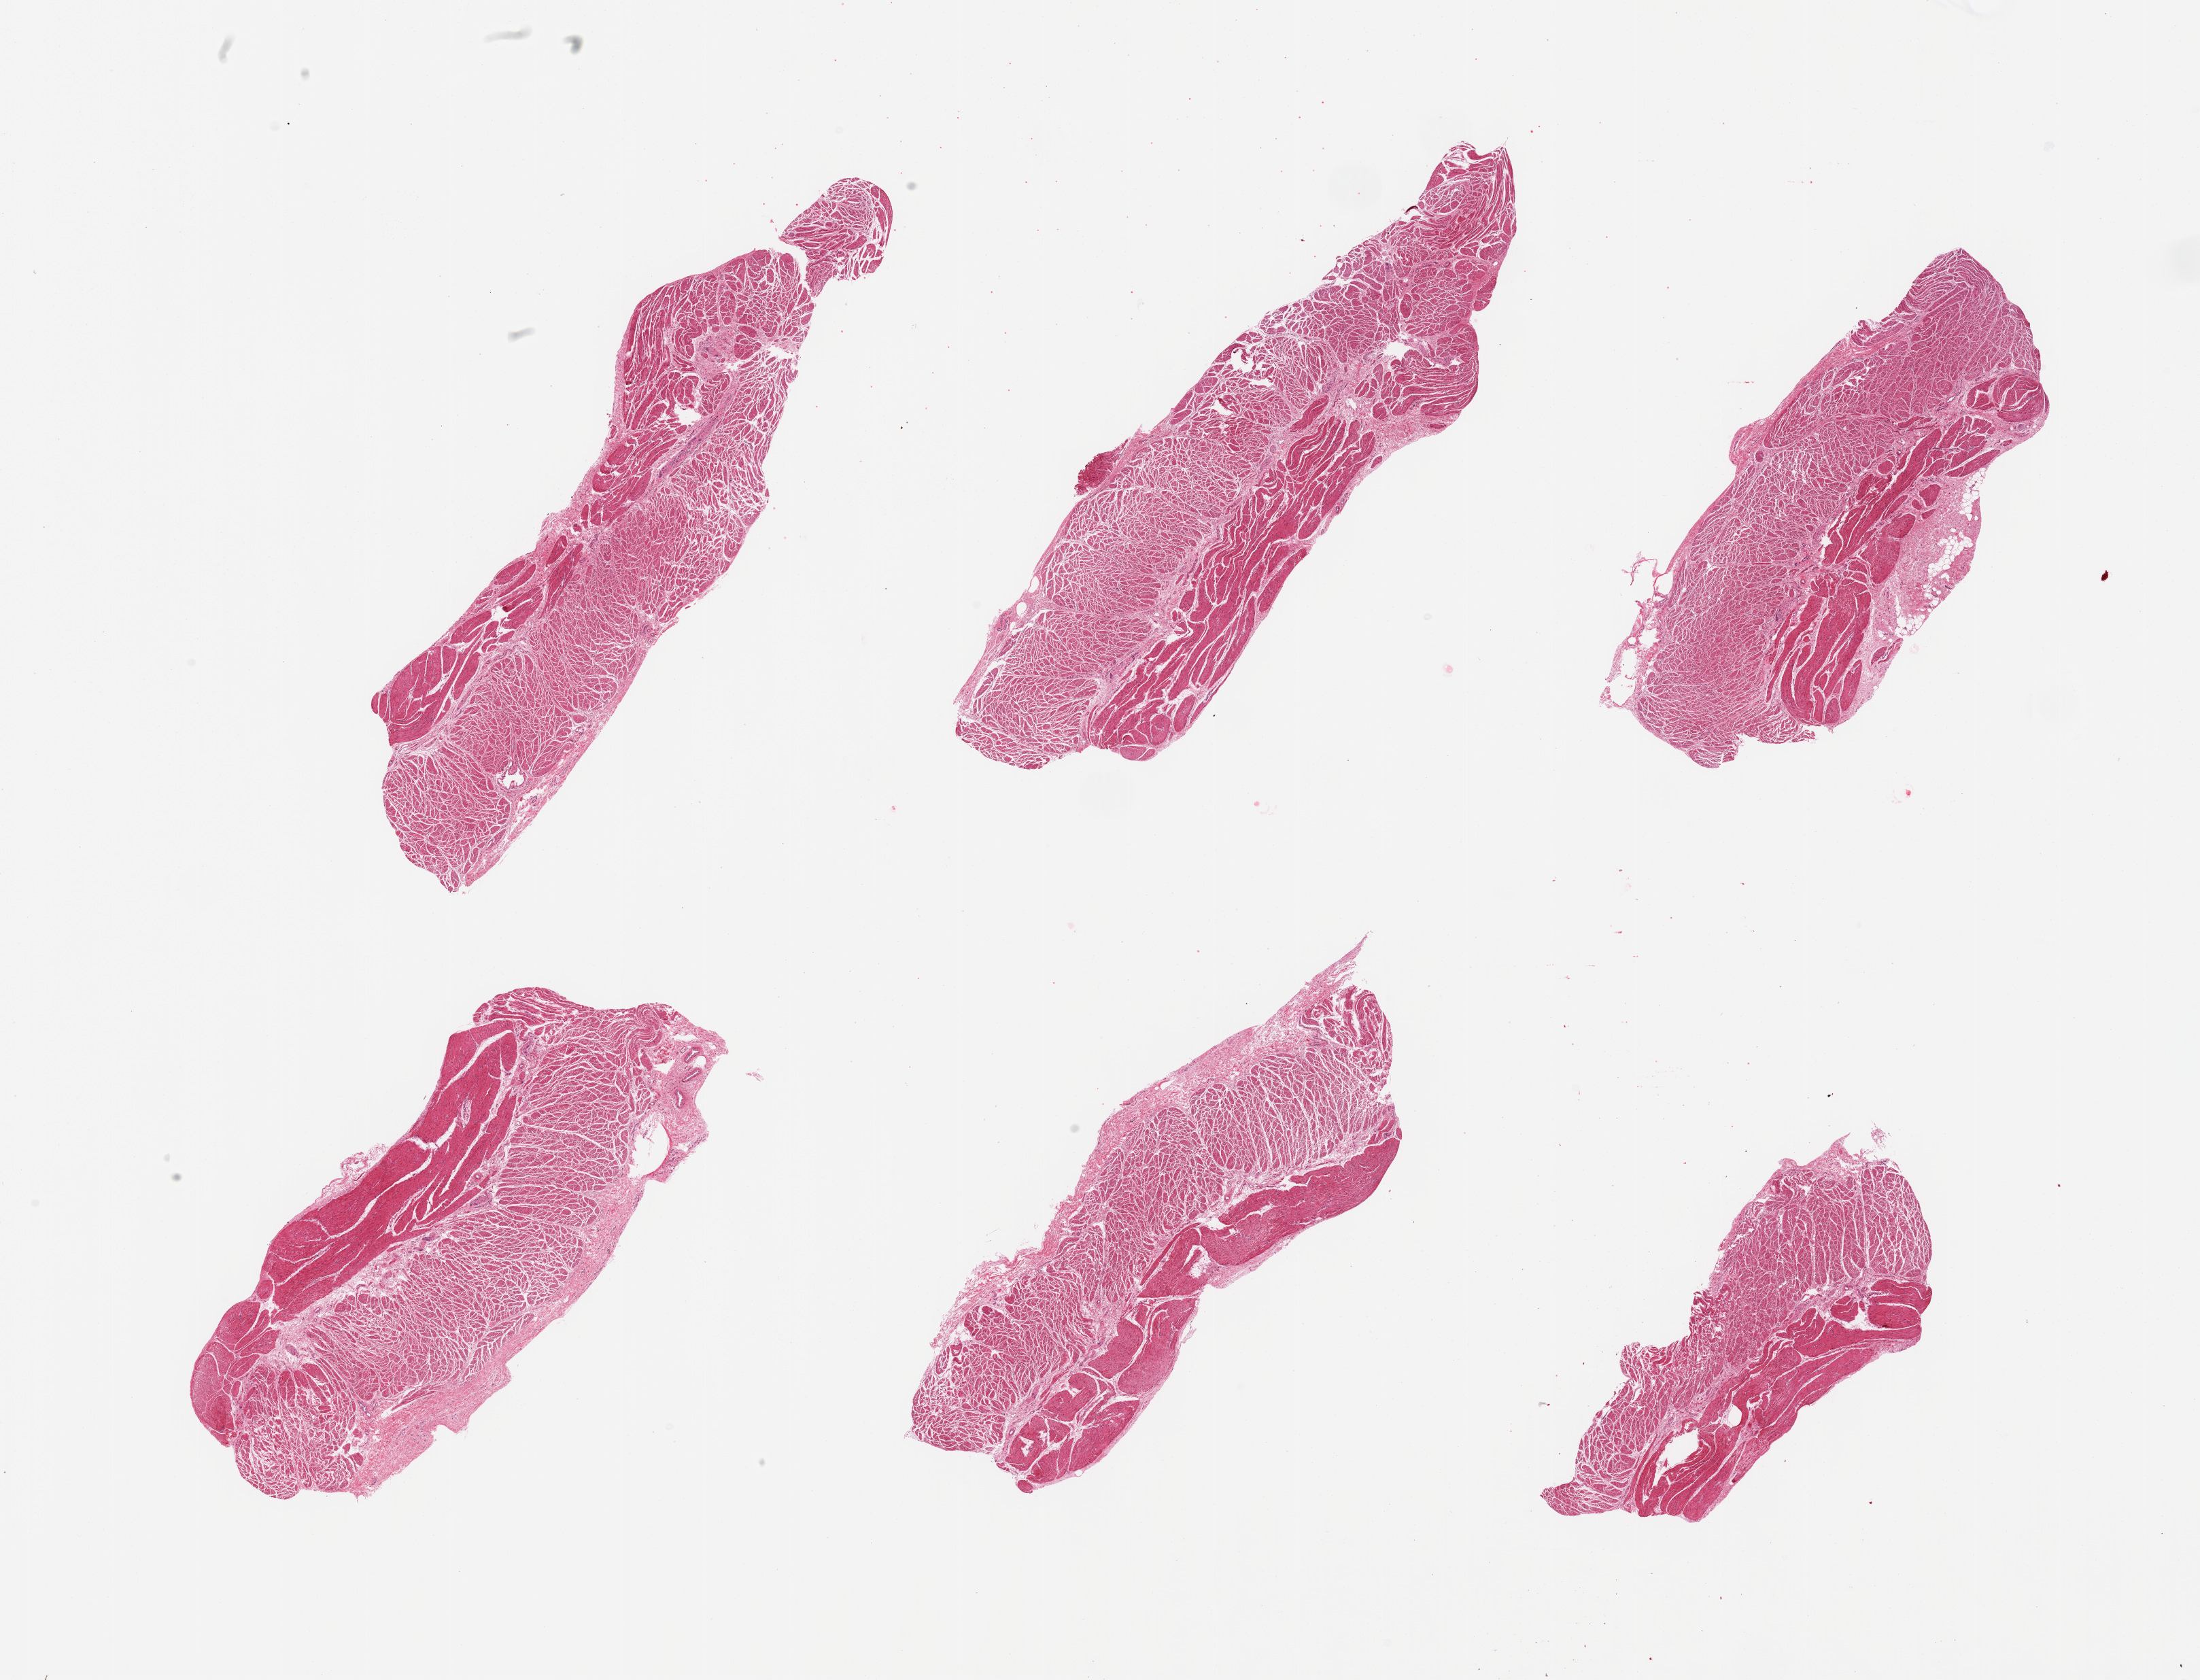
Hematoxylin and eosin (H&E) whole-slide image — a low-resolution overview of the entire scanned area, about 25.6 x 19.5 mm, PAXgene-fixed paraffin-embedded (PFPE) section, target tissue: esophageal muscle, donor tissue sample.
• pathologist's review note for this sample: 6 pieces; target muscularis